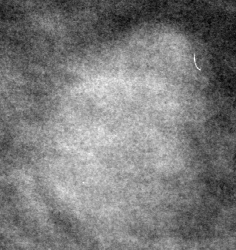
Cropped region of a digitized screen-film mammogram centred on a radiologist-marked abnormality, left breast, MLO view.
- Marked abnormality: mass, shape lobulated, margins circumscribed; BI-RADS assessment category 3; pathology result (as recorded, not read from the image): benign.